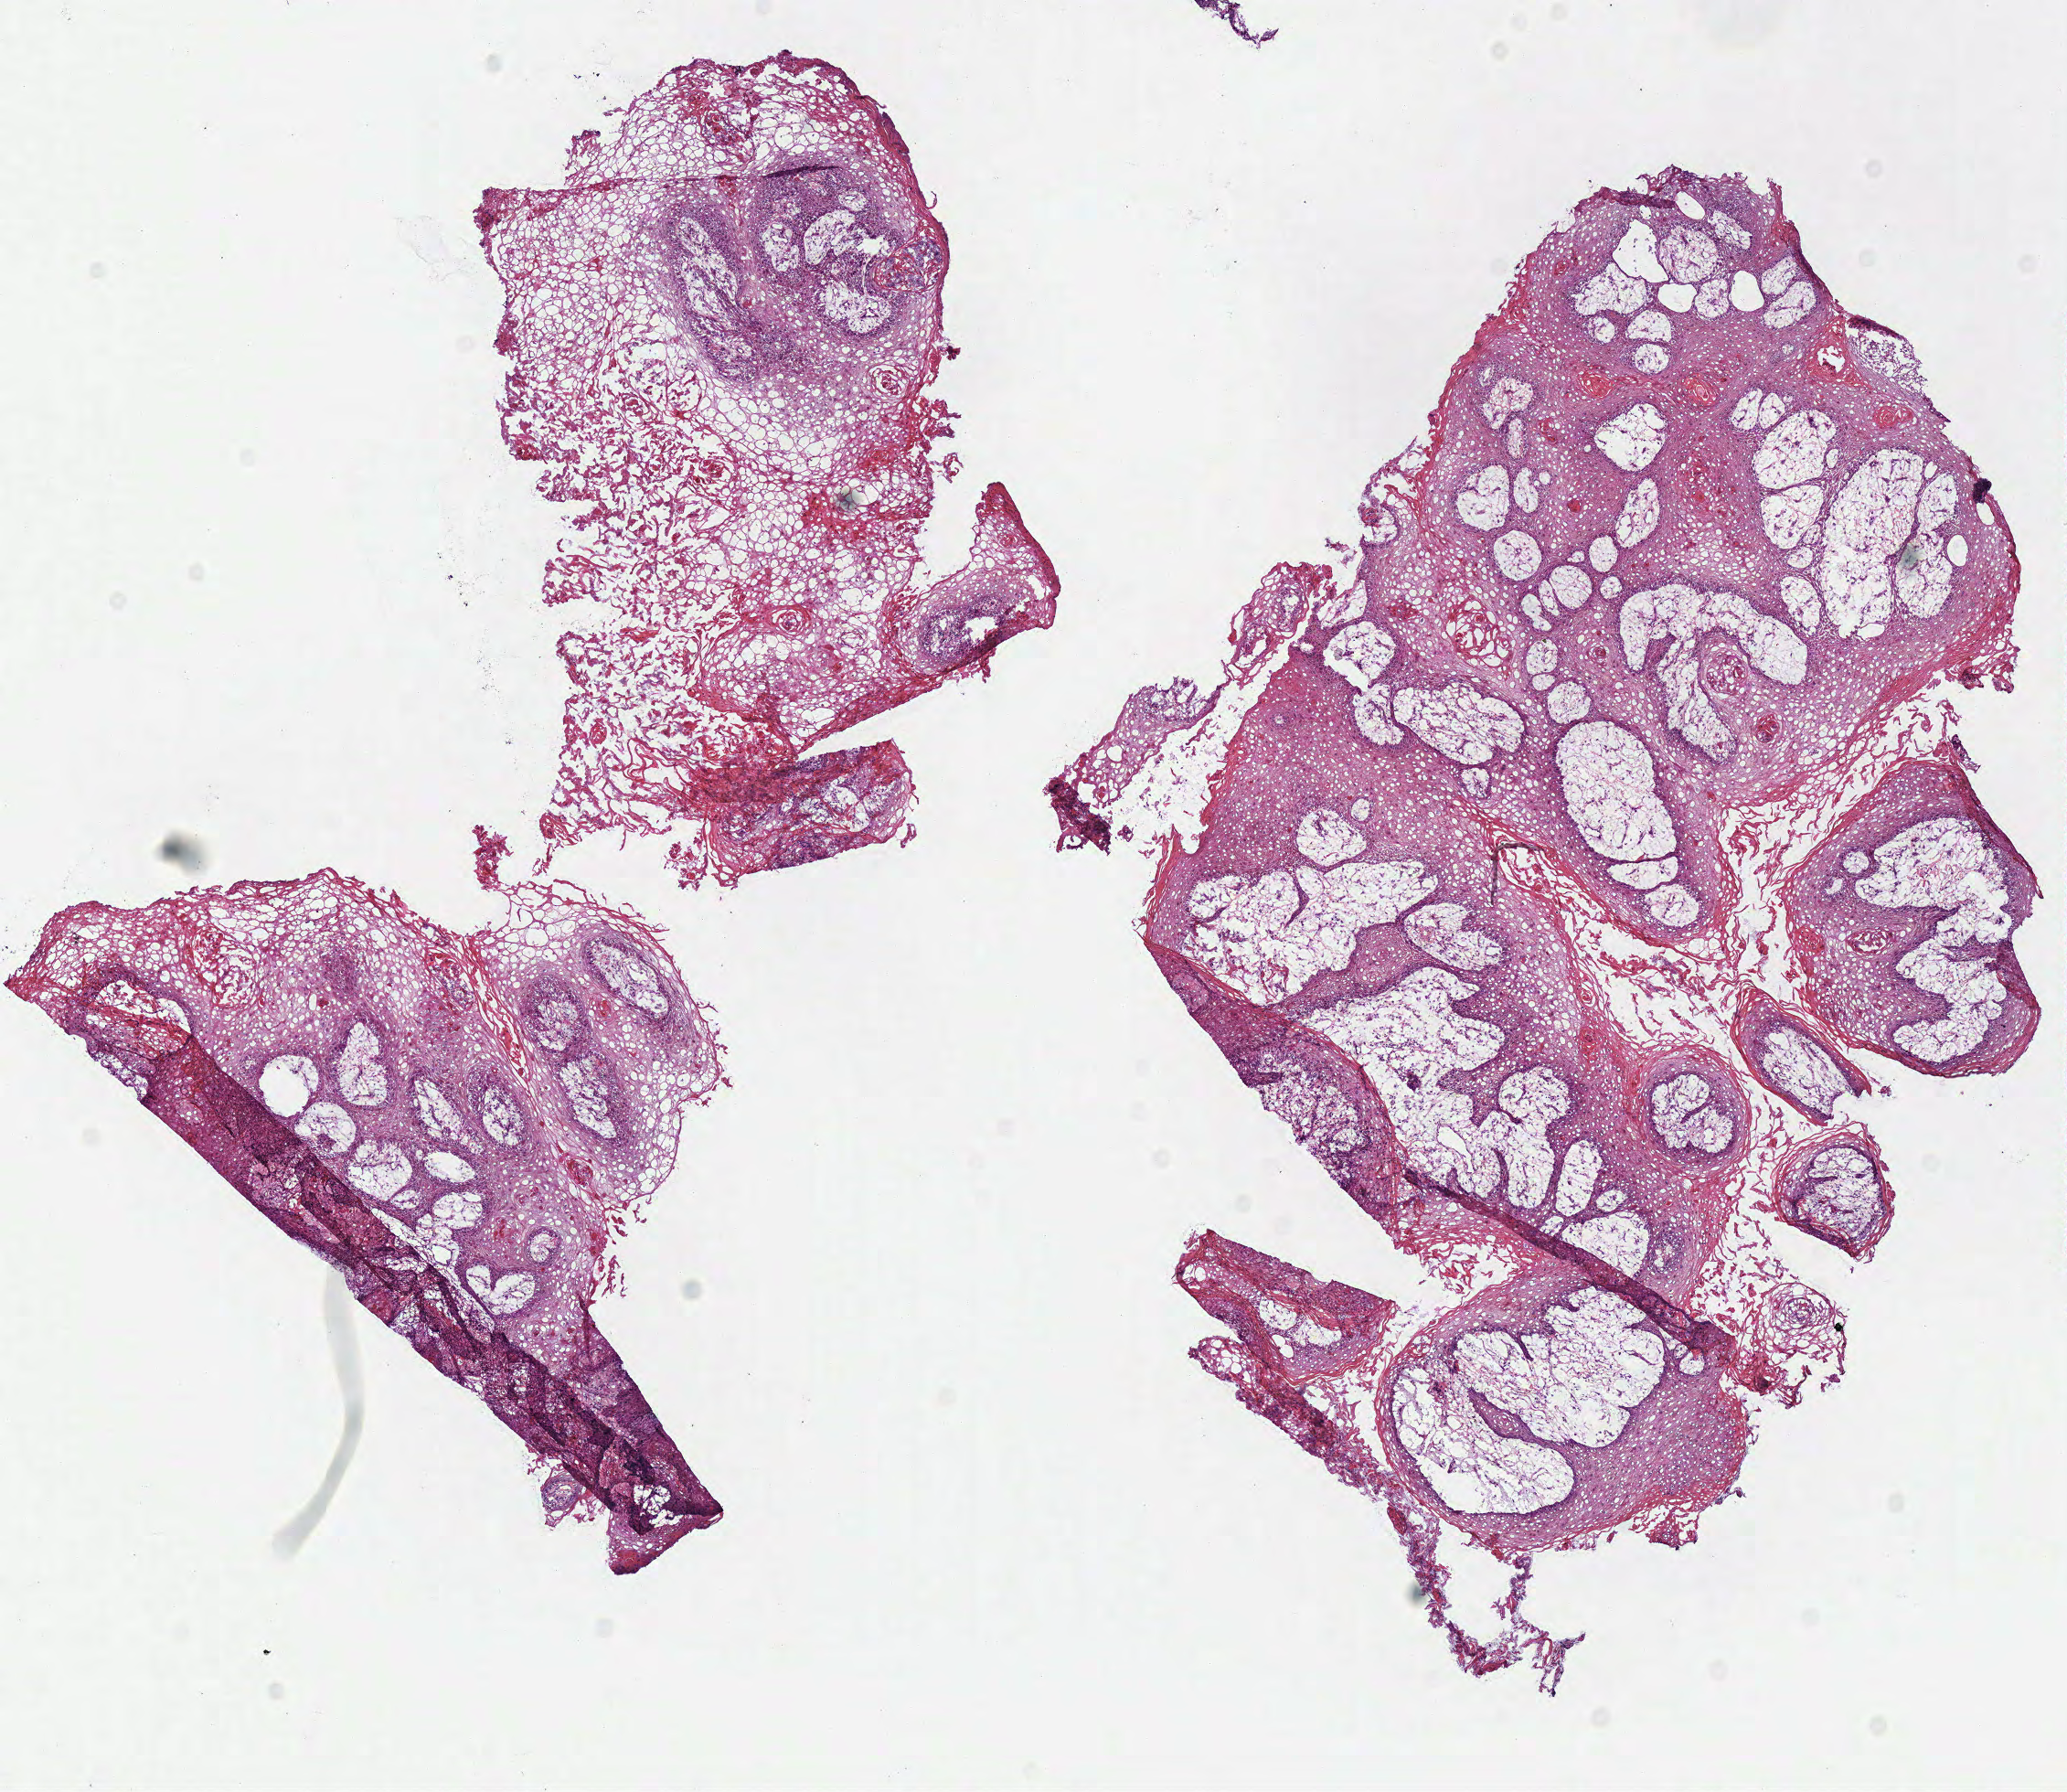
Whole-slide histology image, Hematoxylin and eosin (H&E) stained — shown as a low-resolution overview of the whole scanned area (about 8.9 x 7.7 mm, slide scanned at 40x); frozen section; sample: primary tumour, head and neck. Patient: male, age at initial diagnosis 52 years. Histologic grade: G1 (well differentiated). Composition of this section per pathologist review: tumour cells 75%, tumour nuclei 90%, normal cells 0%, stromal cells 25%, necrosis 0%. Inflammatory infiltration, as recorded: lymphocyte infiltration 1%, monocyte infiltration 0%, neutrophil infiltration 0%.
Histologic diagnosis: Squamous cell carcinoma, NOS (overlapping lesion of lip, oral cavity and pharynx). AJCC pathologic stage: II (7th edition).